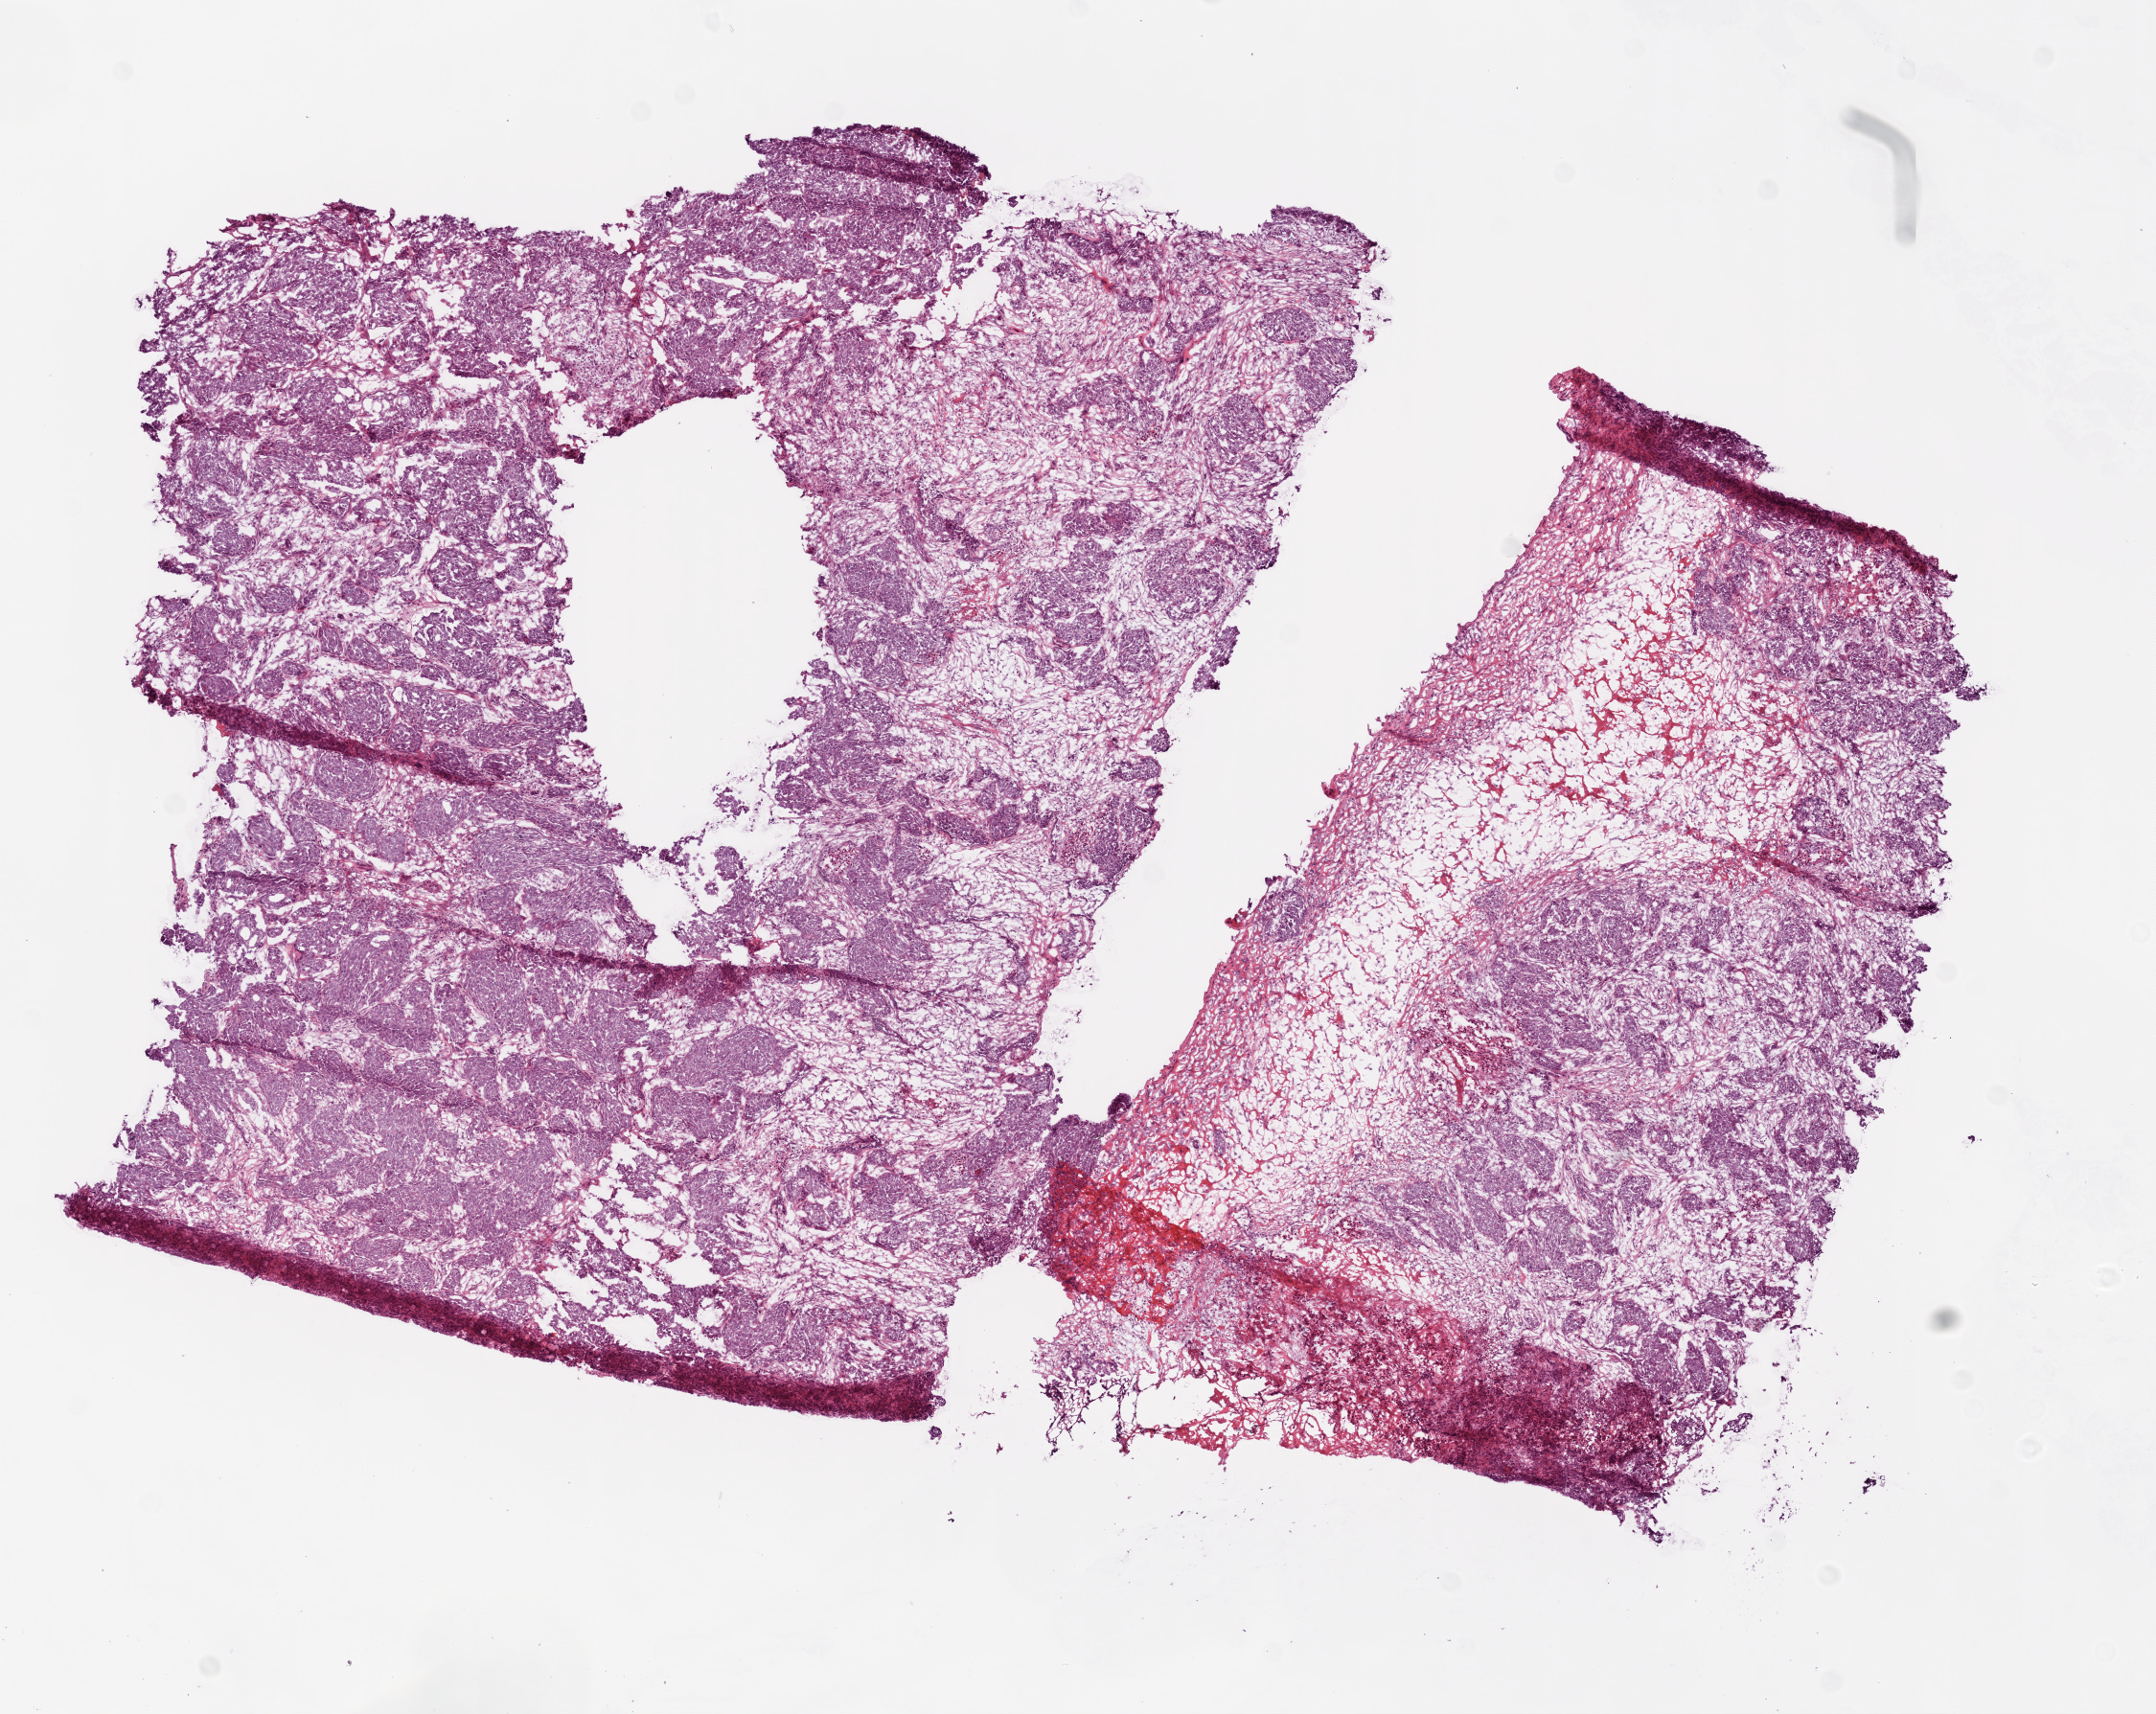
Digitized H&E-stained tissue section (whole slide) — a low-resolution overview of the entire scanned area, about 9.0 x 7.2 mm (slide scanned at 20x); frozen section from the bottom of the tissue portion; primary tumour sample from the ovary. Patient: female, age at initial diagnosis 87 years. Histologic grade: G3 (poorly differentiated). Slide review estimates, as recorded: tumour cells 65%, tumour nuclei 85%, normal cells 0%, stromal cells 35%, necrosis 0%. Inflammatory infiltration, as recorded: lymphocyte infiltration 5%, monocyte infiltration 0%, neutrophil infiltration 0%.
FIGO stage: IIIC. Pathologic diagnosis: Serous cystadenocarcinoma, NOS. Laterality: bilateral.